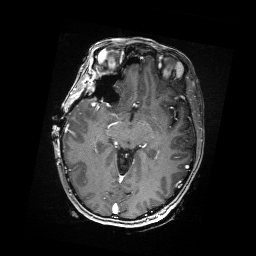
Brain MRI from a brain-tumour surgery series, one axial slice. Position 101 of 176 along the scan axis. T1-weighted post-contrast. 1 mm slice thickness. 256 × 256 image matrix, field of view 256 × 256 mm. From the clinical record (not read from this slice): histopathology: Metastatic Carcinoma from Breast primary; tumour location: Right Frontal.
Annotated regions visible in this slice (outlined manually by an expert reader):
- residual tumour: box from (x=101, y=77) to (x=107, y=84) px